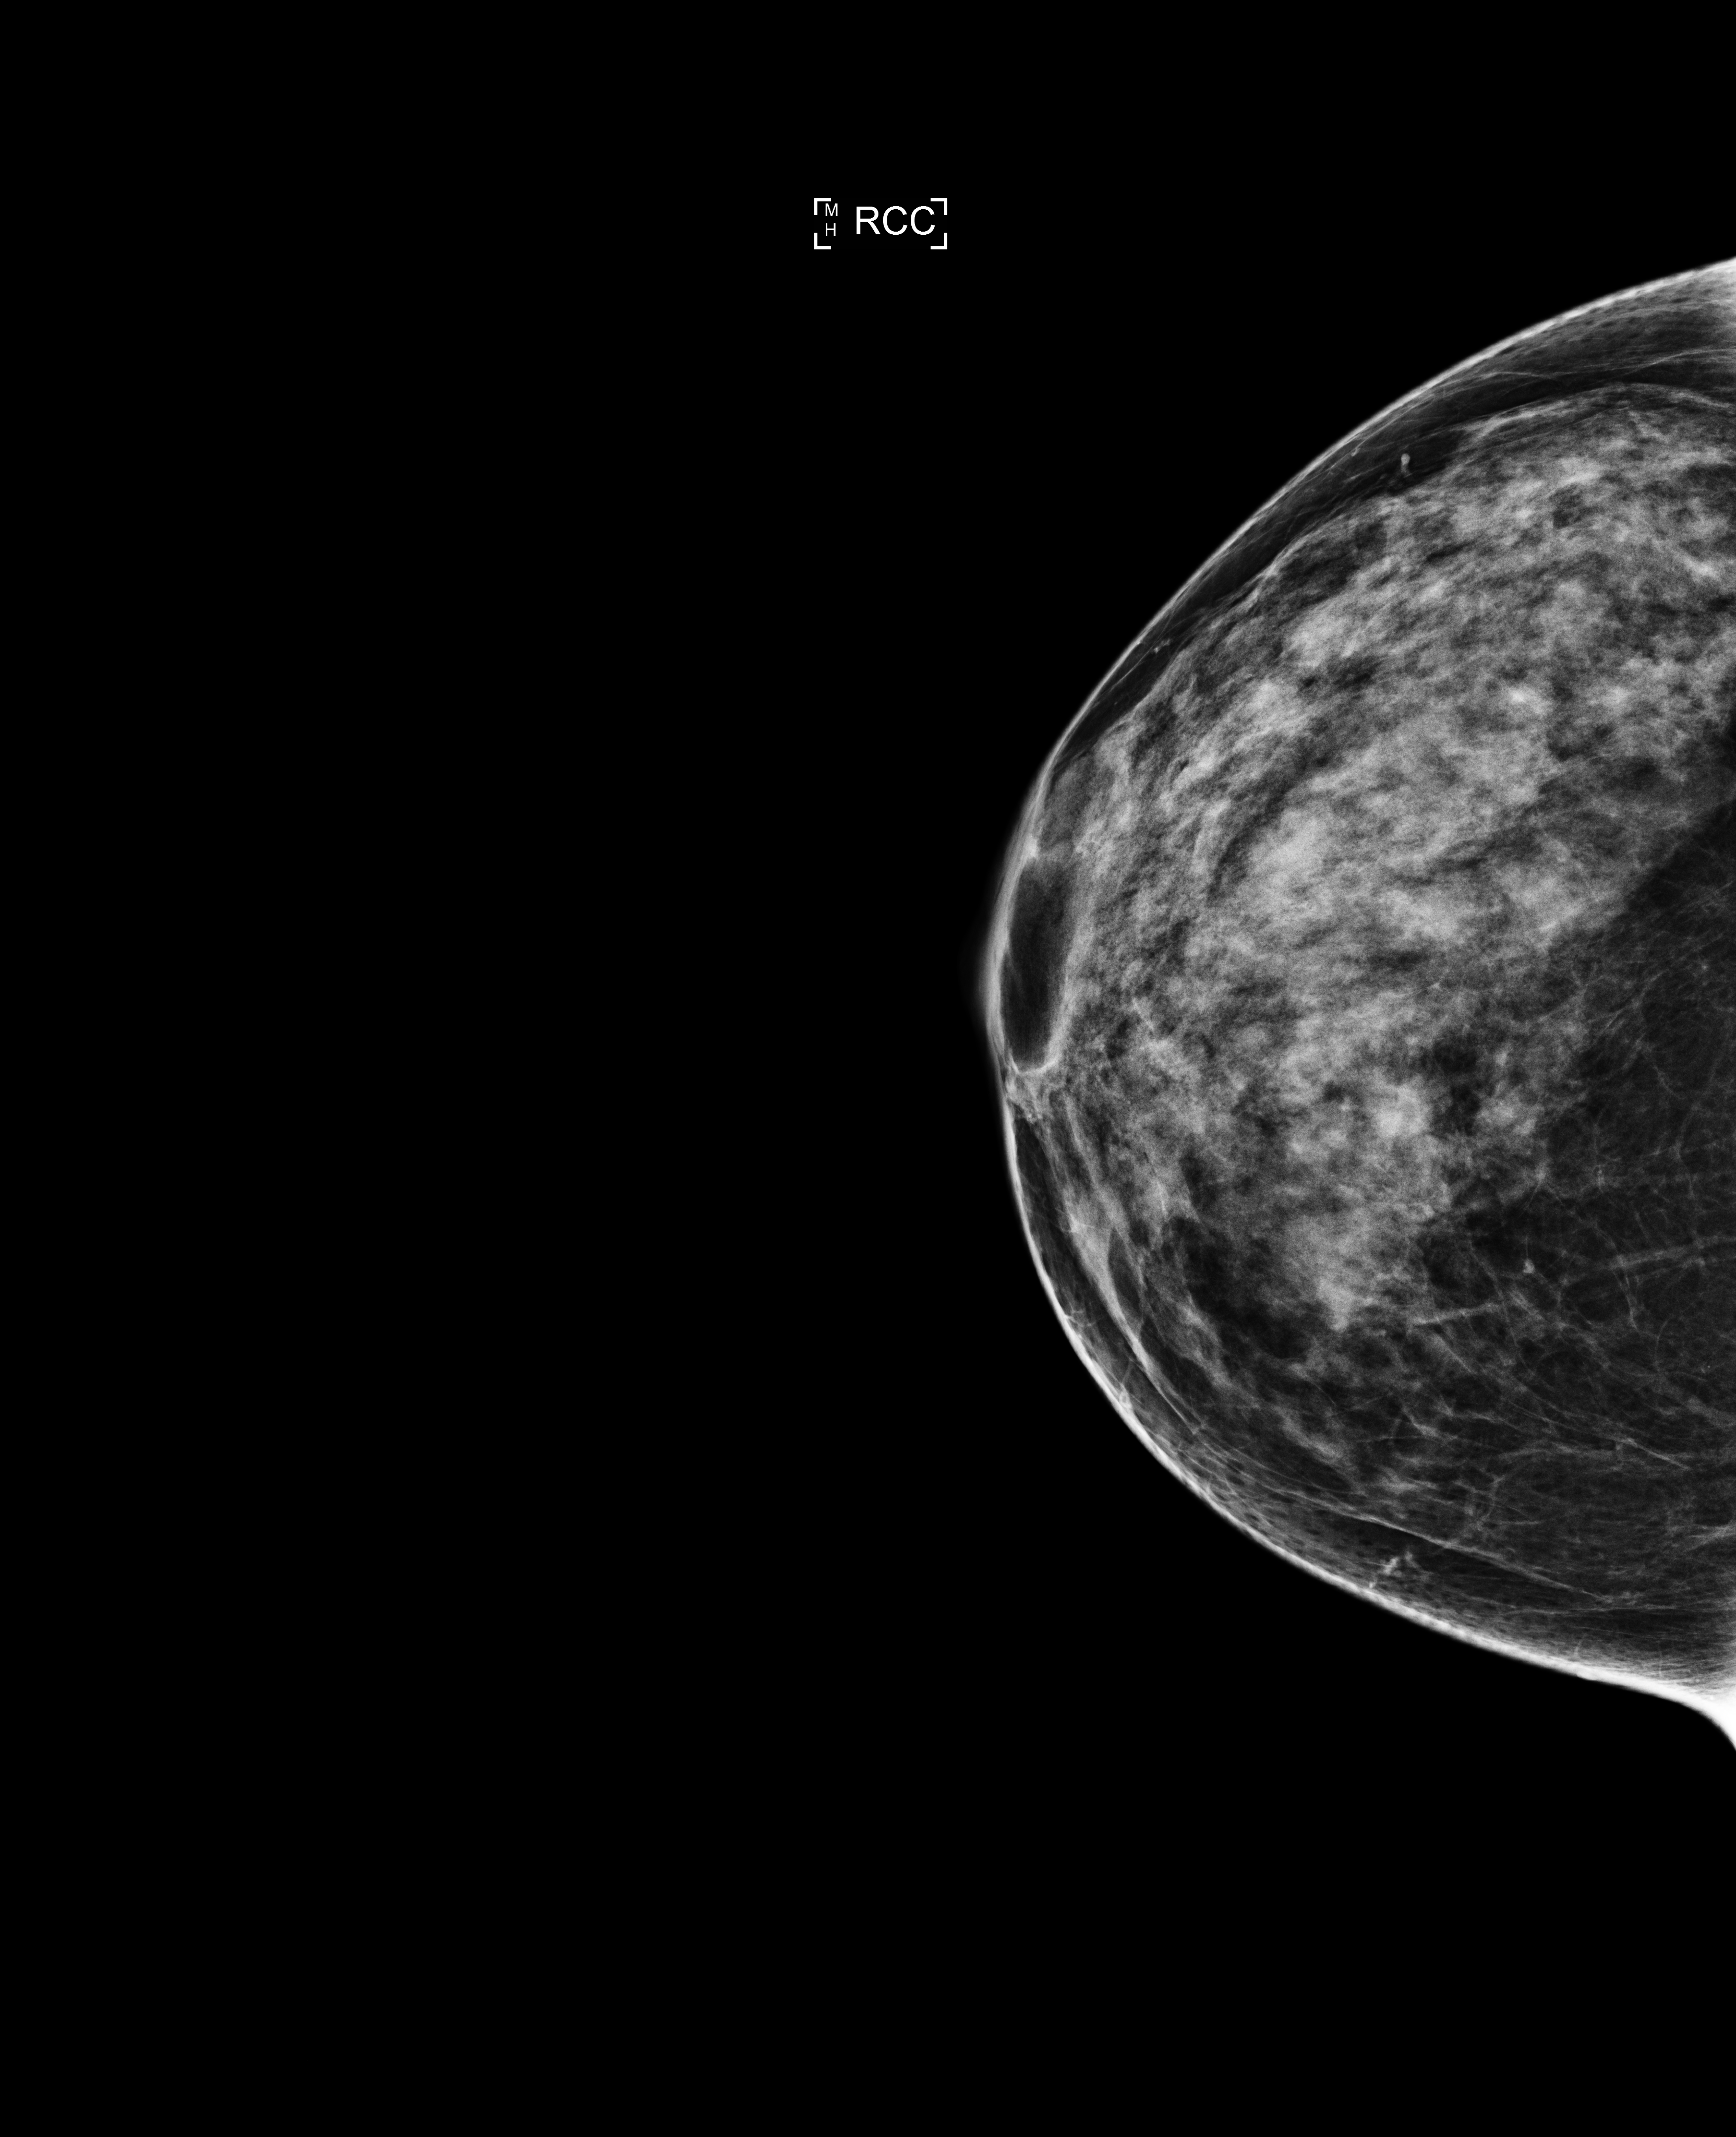
Full-field digital mammogram (FFDM); right breast; CC view; annual screening mammography examination; compressed breast thickness 57 mm. Patient: female, 41 years.
Breast density at the screening exam (both breasts): extremely dense (BI-RADS density category d). Final BI-RADS category for the screening round (tomosynthesis exam, both breasts): category 1. Recall: no recall after this screen.